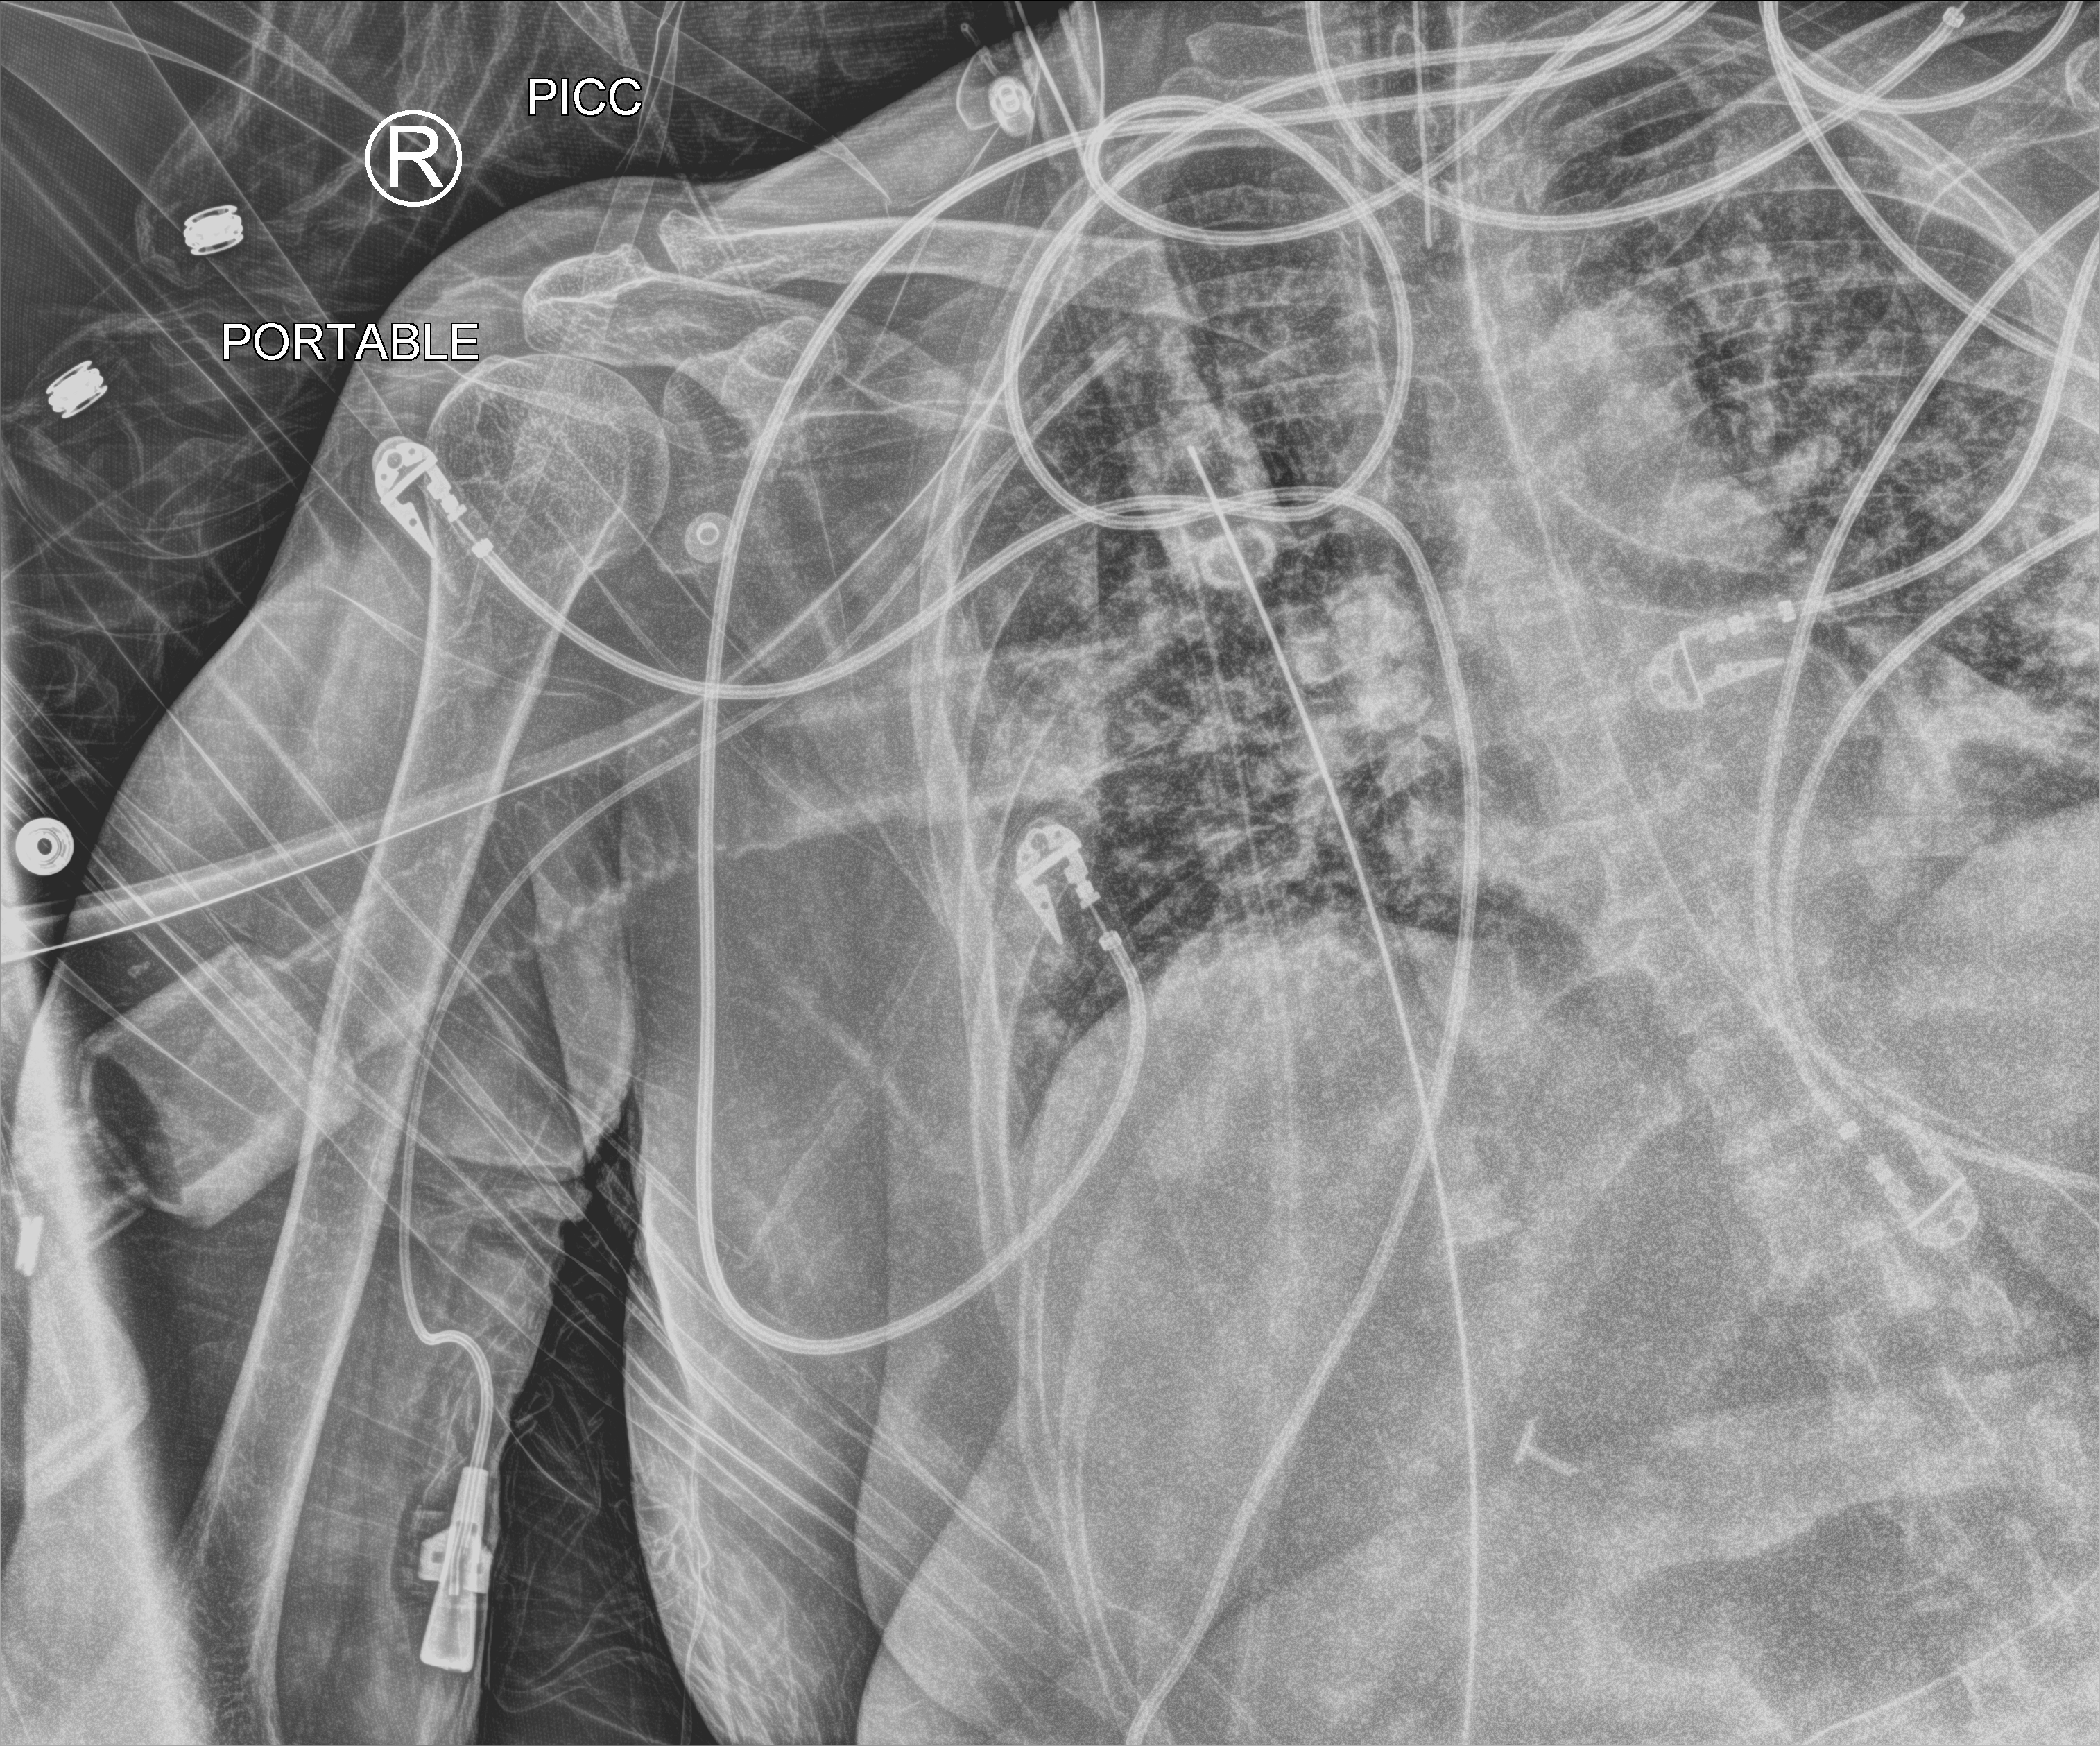
Portable chest radiograph. Patient hospitalised with COVID-19; female, aged 18–59 years.
Admission-level facts for this patient (not findings on this image; timing relative to this image not recorded): mechanically ventilated during this hospital stay: yes.